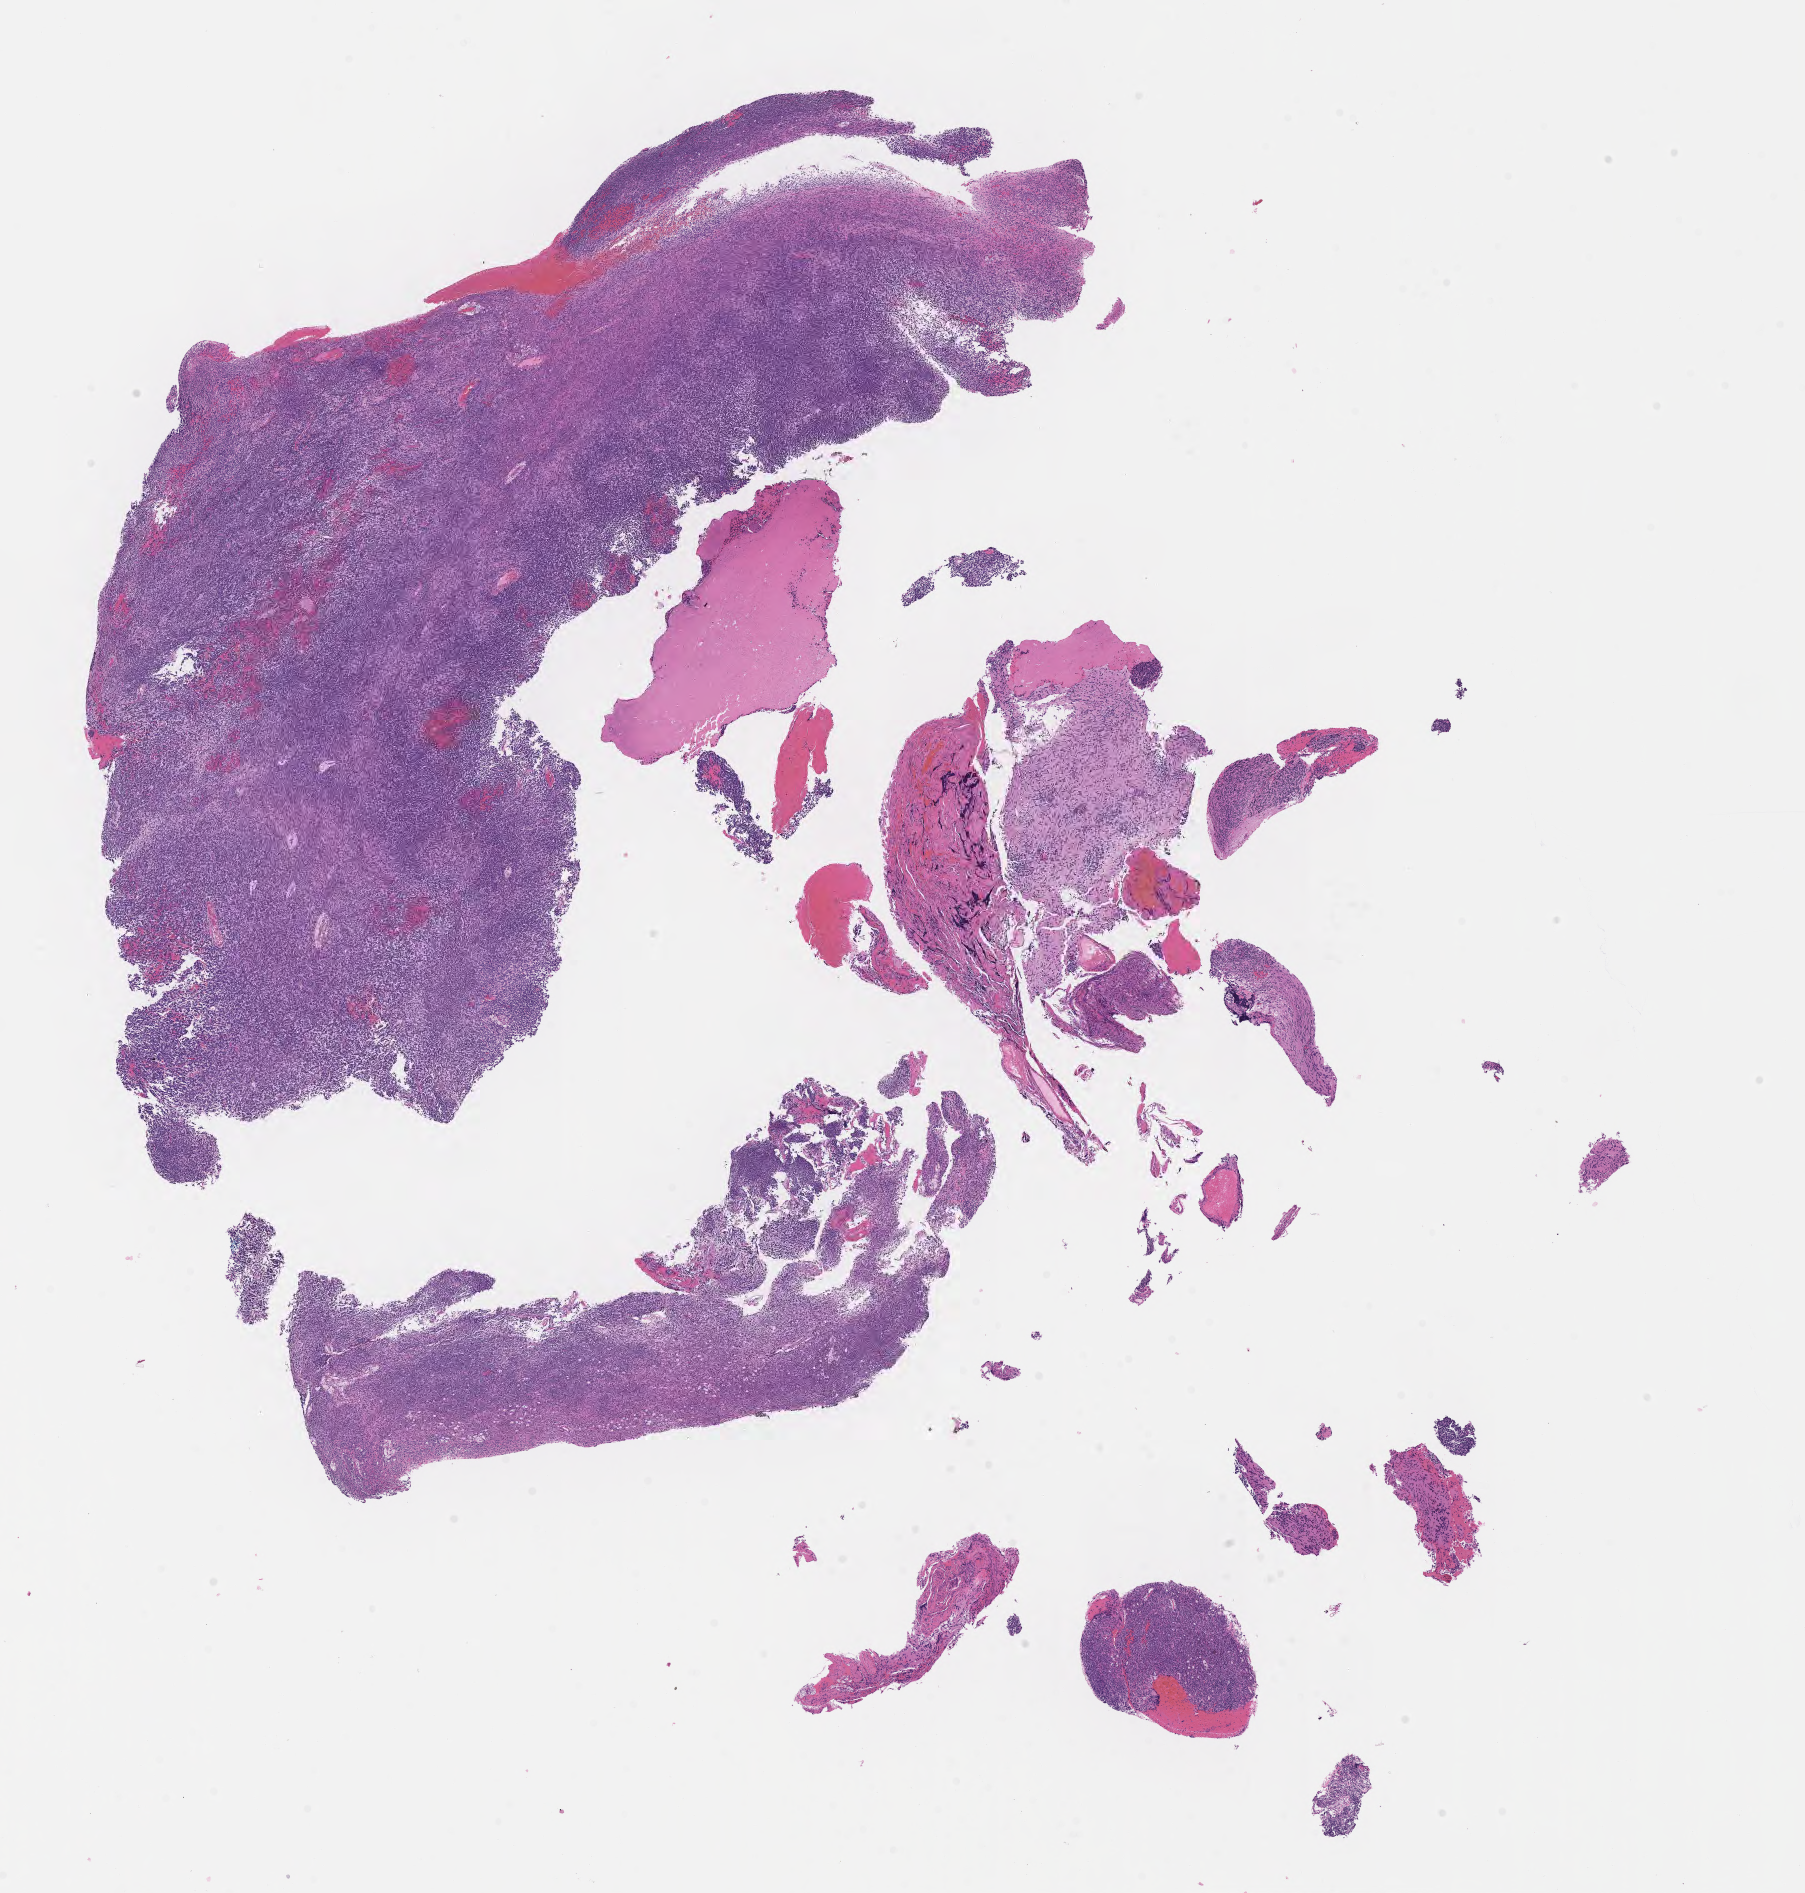
Whole-slide image, H&E stain of tumor tissue from the brain, whole scanned area (about 14.6 x 15.3 mm) shown as a low-resolution overview; formalin-fixed, paraffin-embedded (FFPE) tissue. Patient female; age 56 months (4 years 8 months).
Diagnosis: Neoplasm, malignant, uncertain whether primary or metastatic.